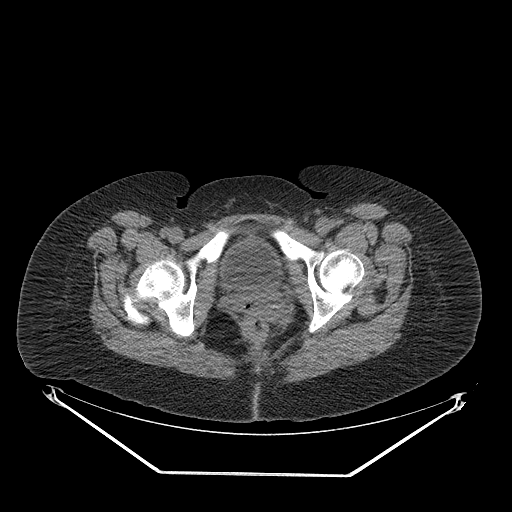
CT of an extremity soft-tissue mass (from a PET/CT study), one axial slice. Slice 57 of 267 in the series (ordered by position). Reconstruction kernel STANDARD. 140 kVp. Soft-tissue window (W 400 / L 40 HU). 3.75 mm slice thickness. 512 × 512 image matrix, field of view 500 × 500 mm. Female patient. From the clinical record (not read from this slice): histological type: myxofibrosarcoma; grade: intermediate; site of the primary tumour: left thigh.
Annotated regions visible in this slice (expert contour drawn on MRI and transferred to this co-registered scan by the dataset authors):
- gross tumour volume including surrounding oedema: box from (x=283, y=224) to (x=353, y=250) px